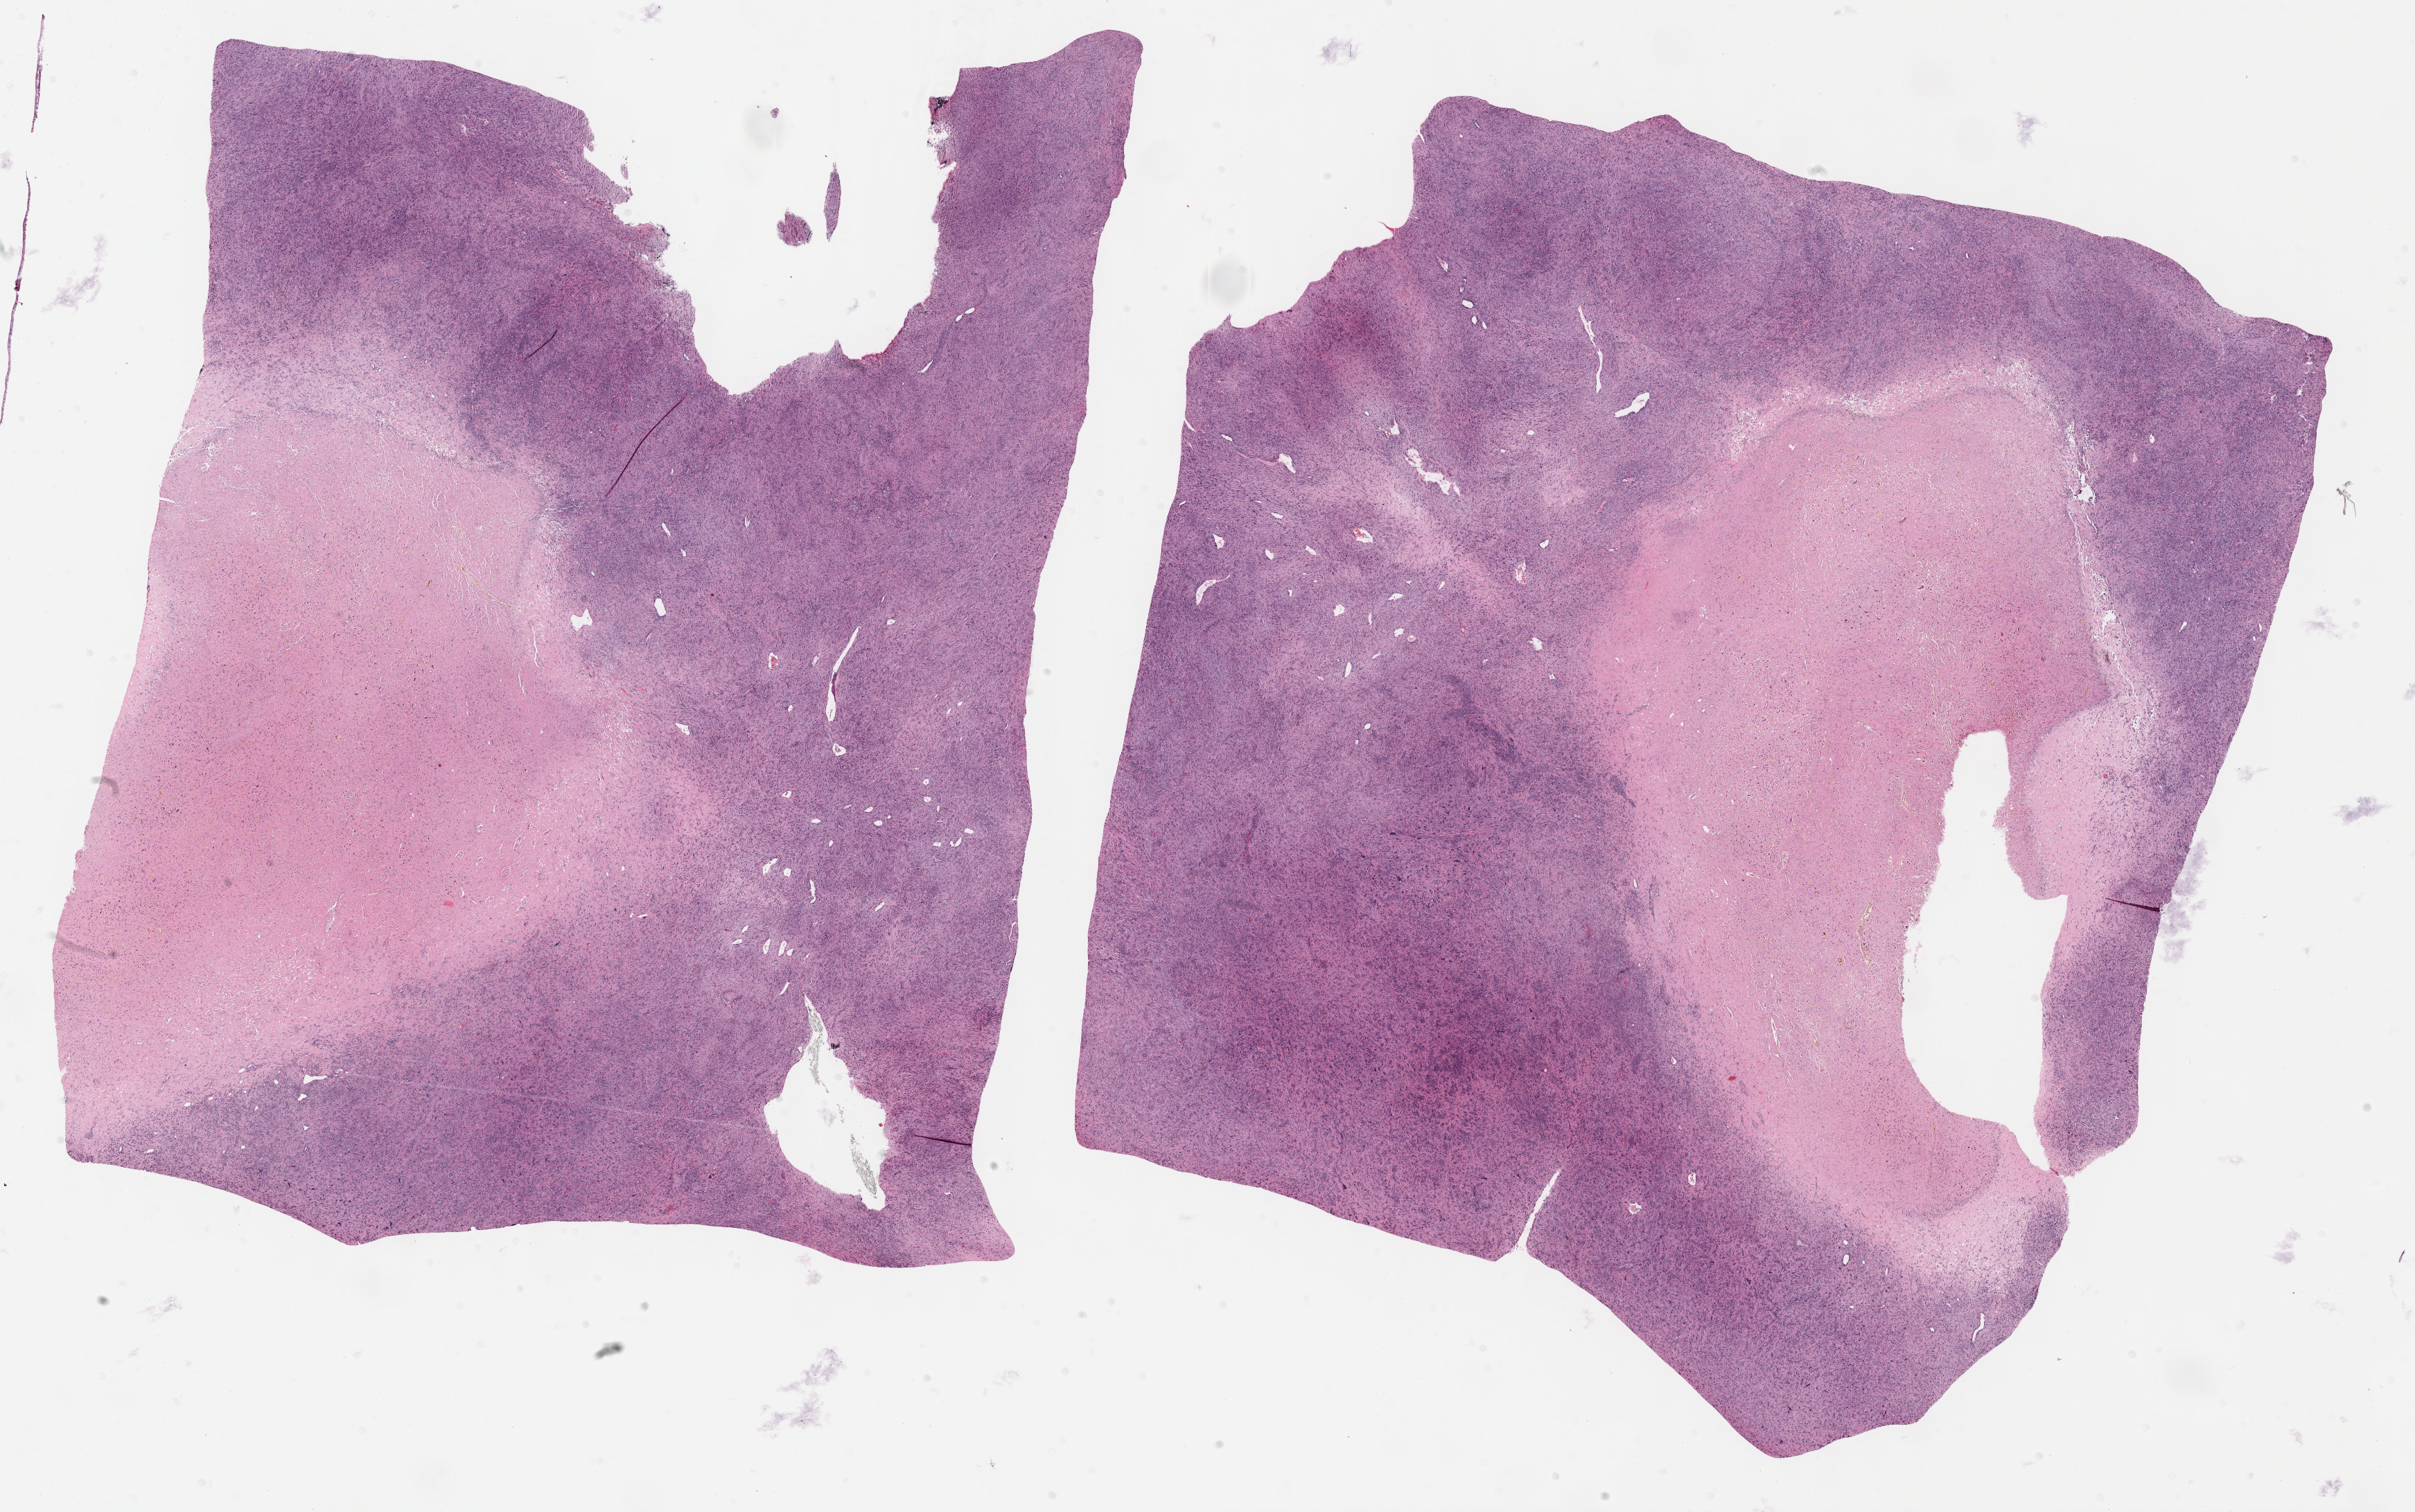
Digitized H&E-stained tissue section (whole slide) — low-resolution overview of the scanned area, about 28.2 x 17.6 mm (acquisition: 40x scan). FFPE section. Connective, subcutaneous and other soft tissues, primary tumour sample. Patient sex: female.
Diagnosis: Malignant fibrous histiocytoma (connective, subcutaneous and other soft tissues of trunk, NOS).